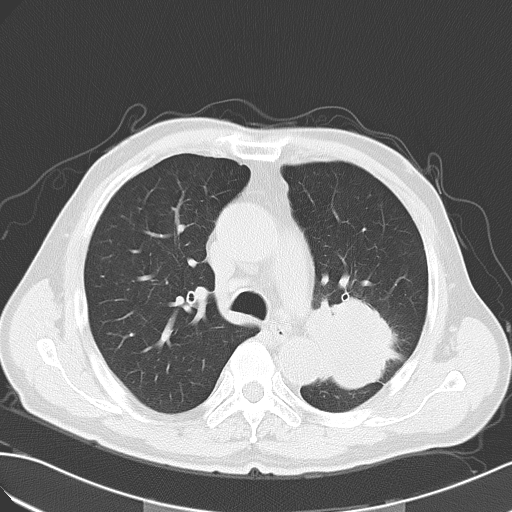
Chest CT, one axial slice. Position 37 of 55 along the scan axis. Reconstruction kernel B70f. 120 kVp. Lung window (W 1500 / L -600 HU). 5 mm slice thickness. 512 × 512 image matrix. Male patient, age 63 years. Case-level facts recorded for this patient, not image findings: clinical TNM (as recorded): T3 N3 M1a.
Structures marked on this image (rectangle marked by the reading radiologist):
- lung tumour (recorded histology: large cell carcinoma): bounding box <309,293,399,395> (left, top, right, bottom; pixels)